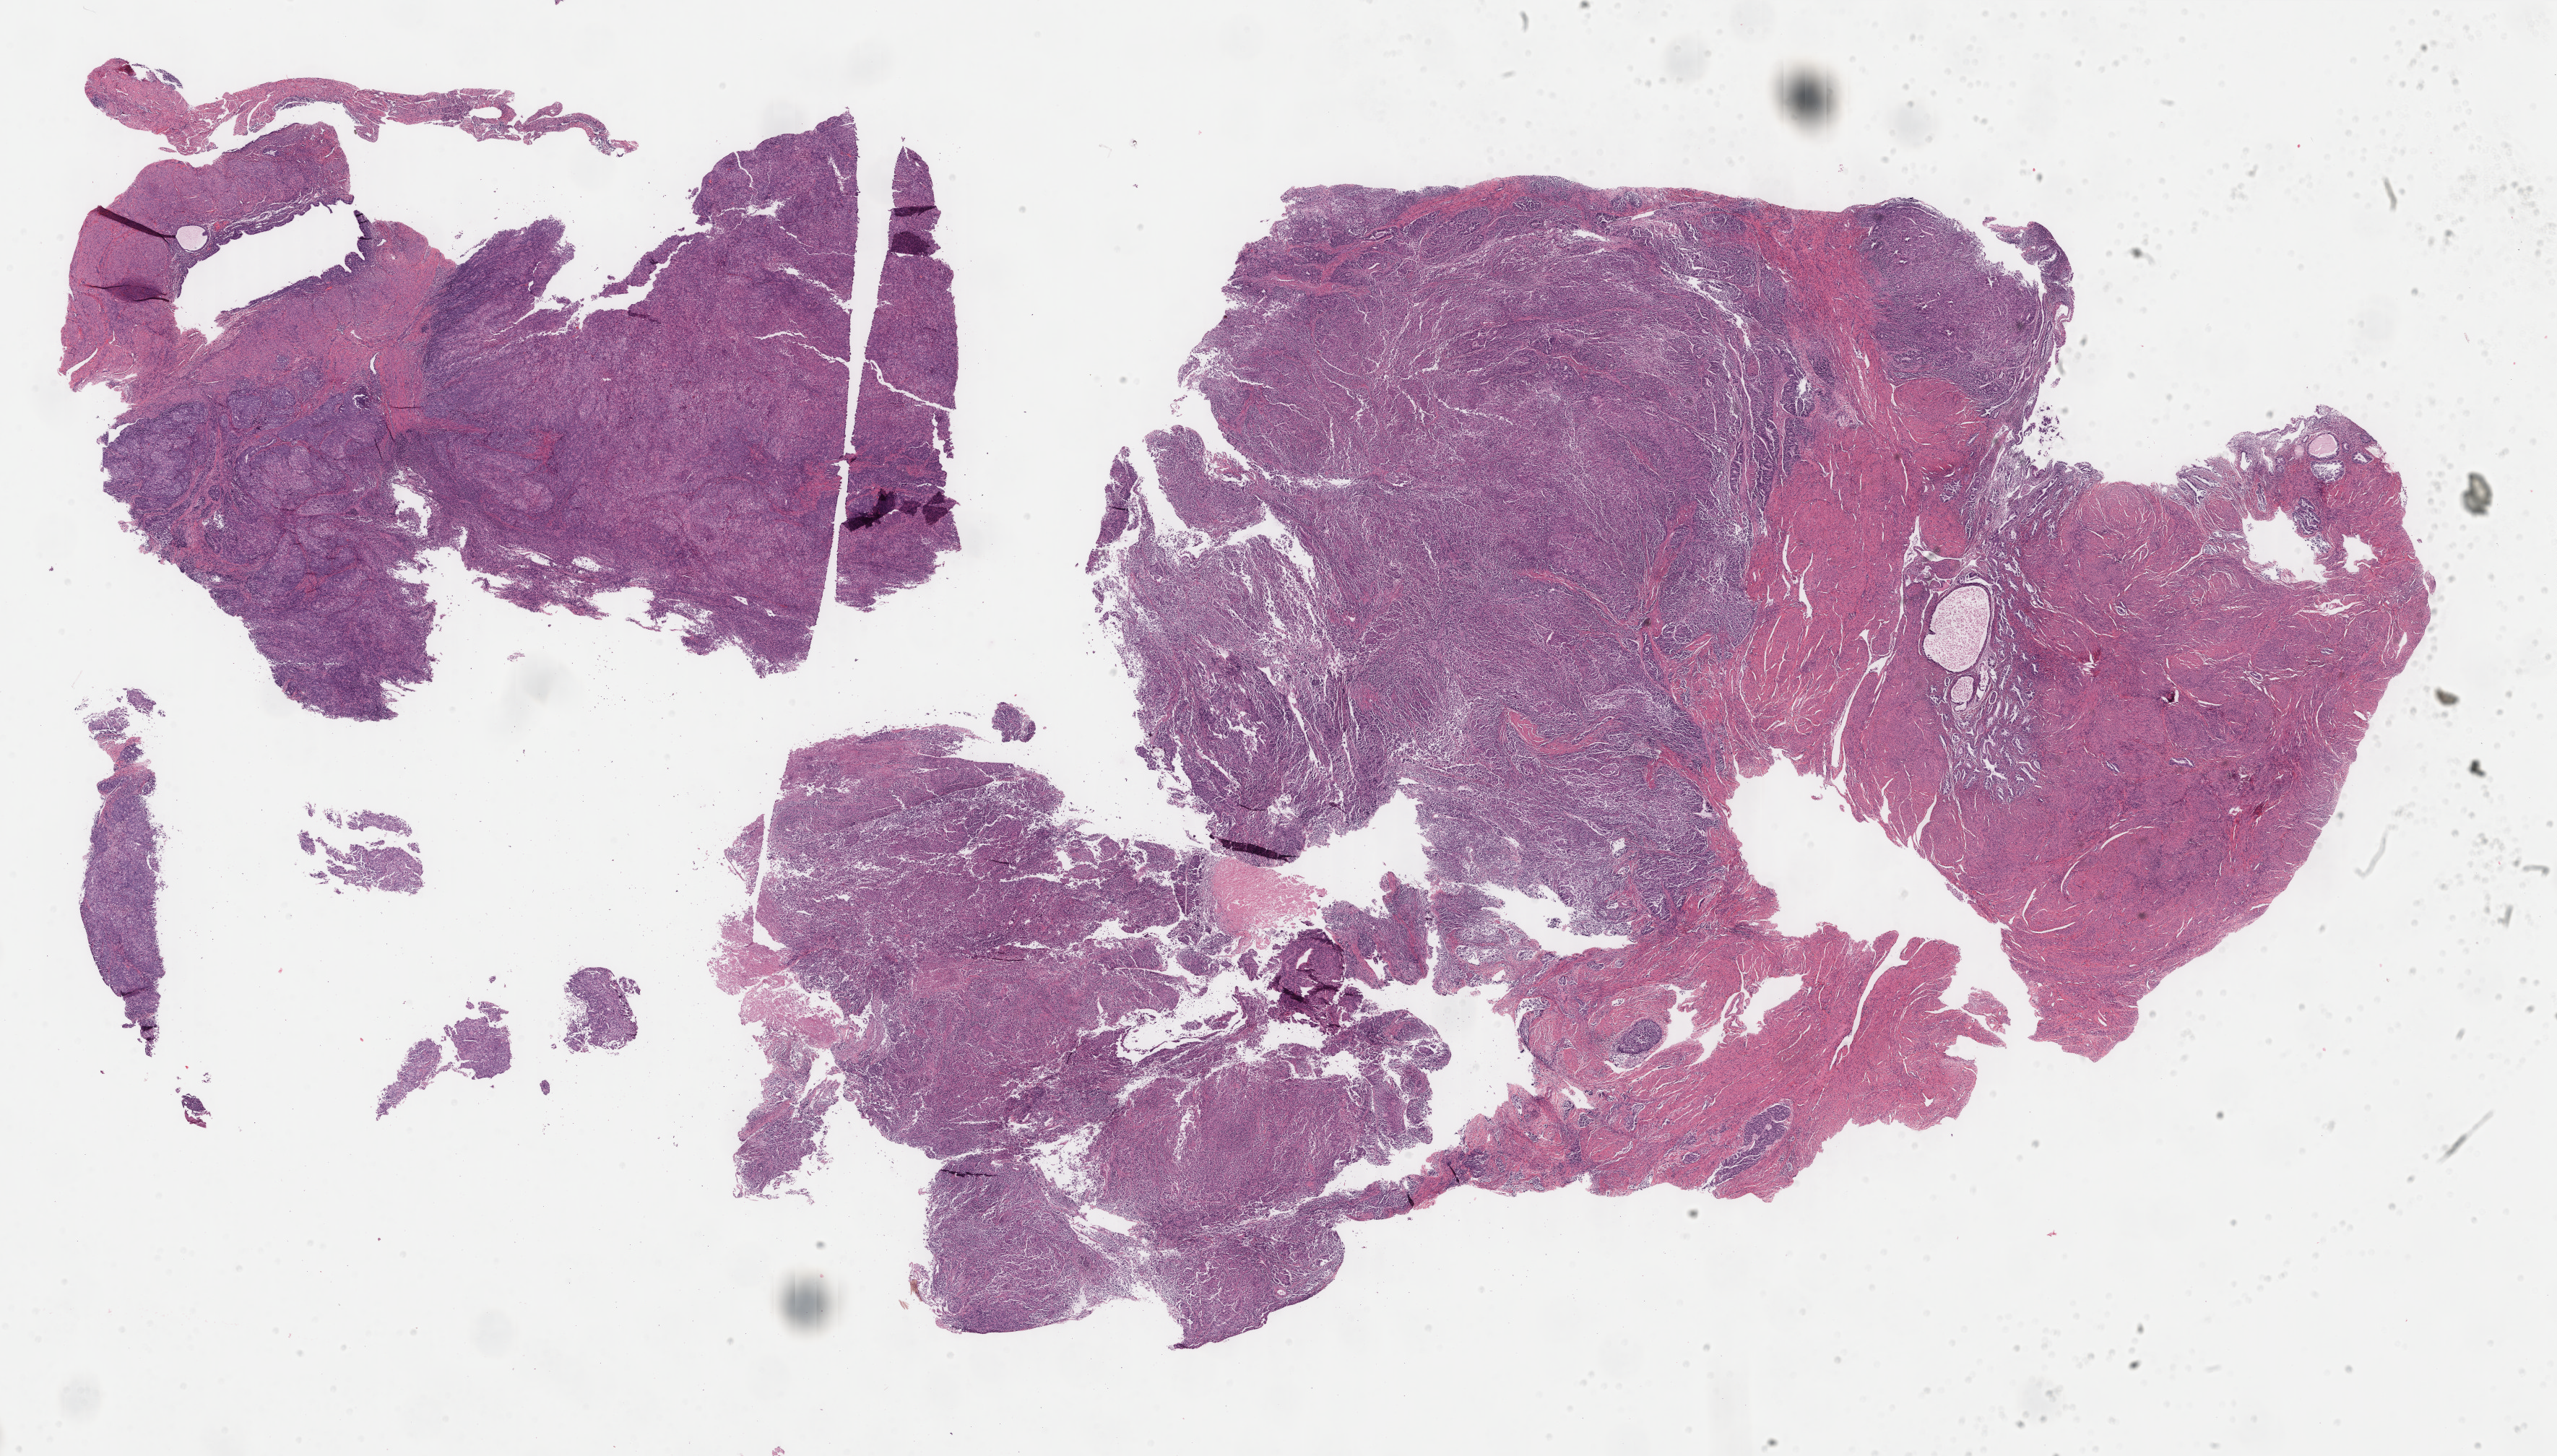
Digitized Hematoxylin and eosin (H&E) stained tissue section (whole slide) — shown as a low-resolution overview of the whole scanned area (about 28.1 x 16.0 mm, from a 40x scan); formalin-fixed paraffin-embedded (FFPE) diagnostic section; uterus, primary tumour sample. Female, age 78 years at initial diagnosis. Histologic grade: G3 (poorly differentiated).
• FIGO stage: IIIC
• diagnosis: Endometrioid adenocarcinoma, NOS
• lymph nodes positive (case pathology): 7 of 30 examined